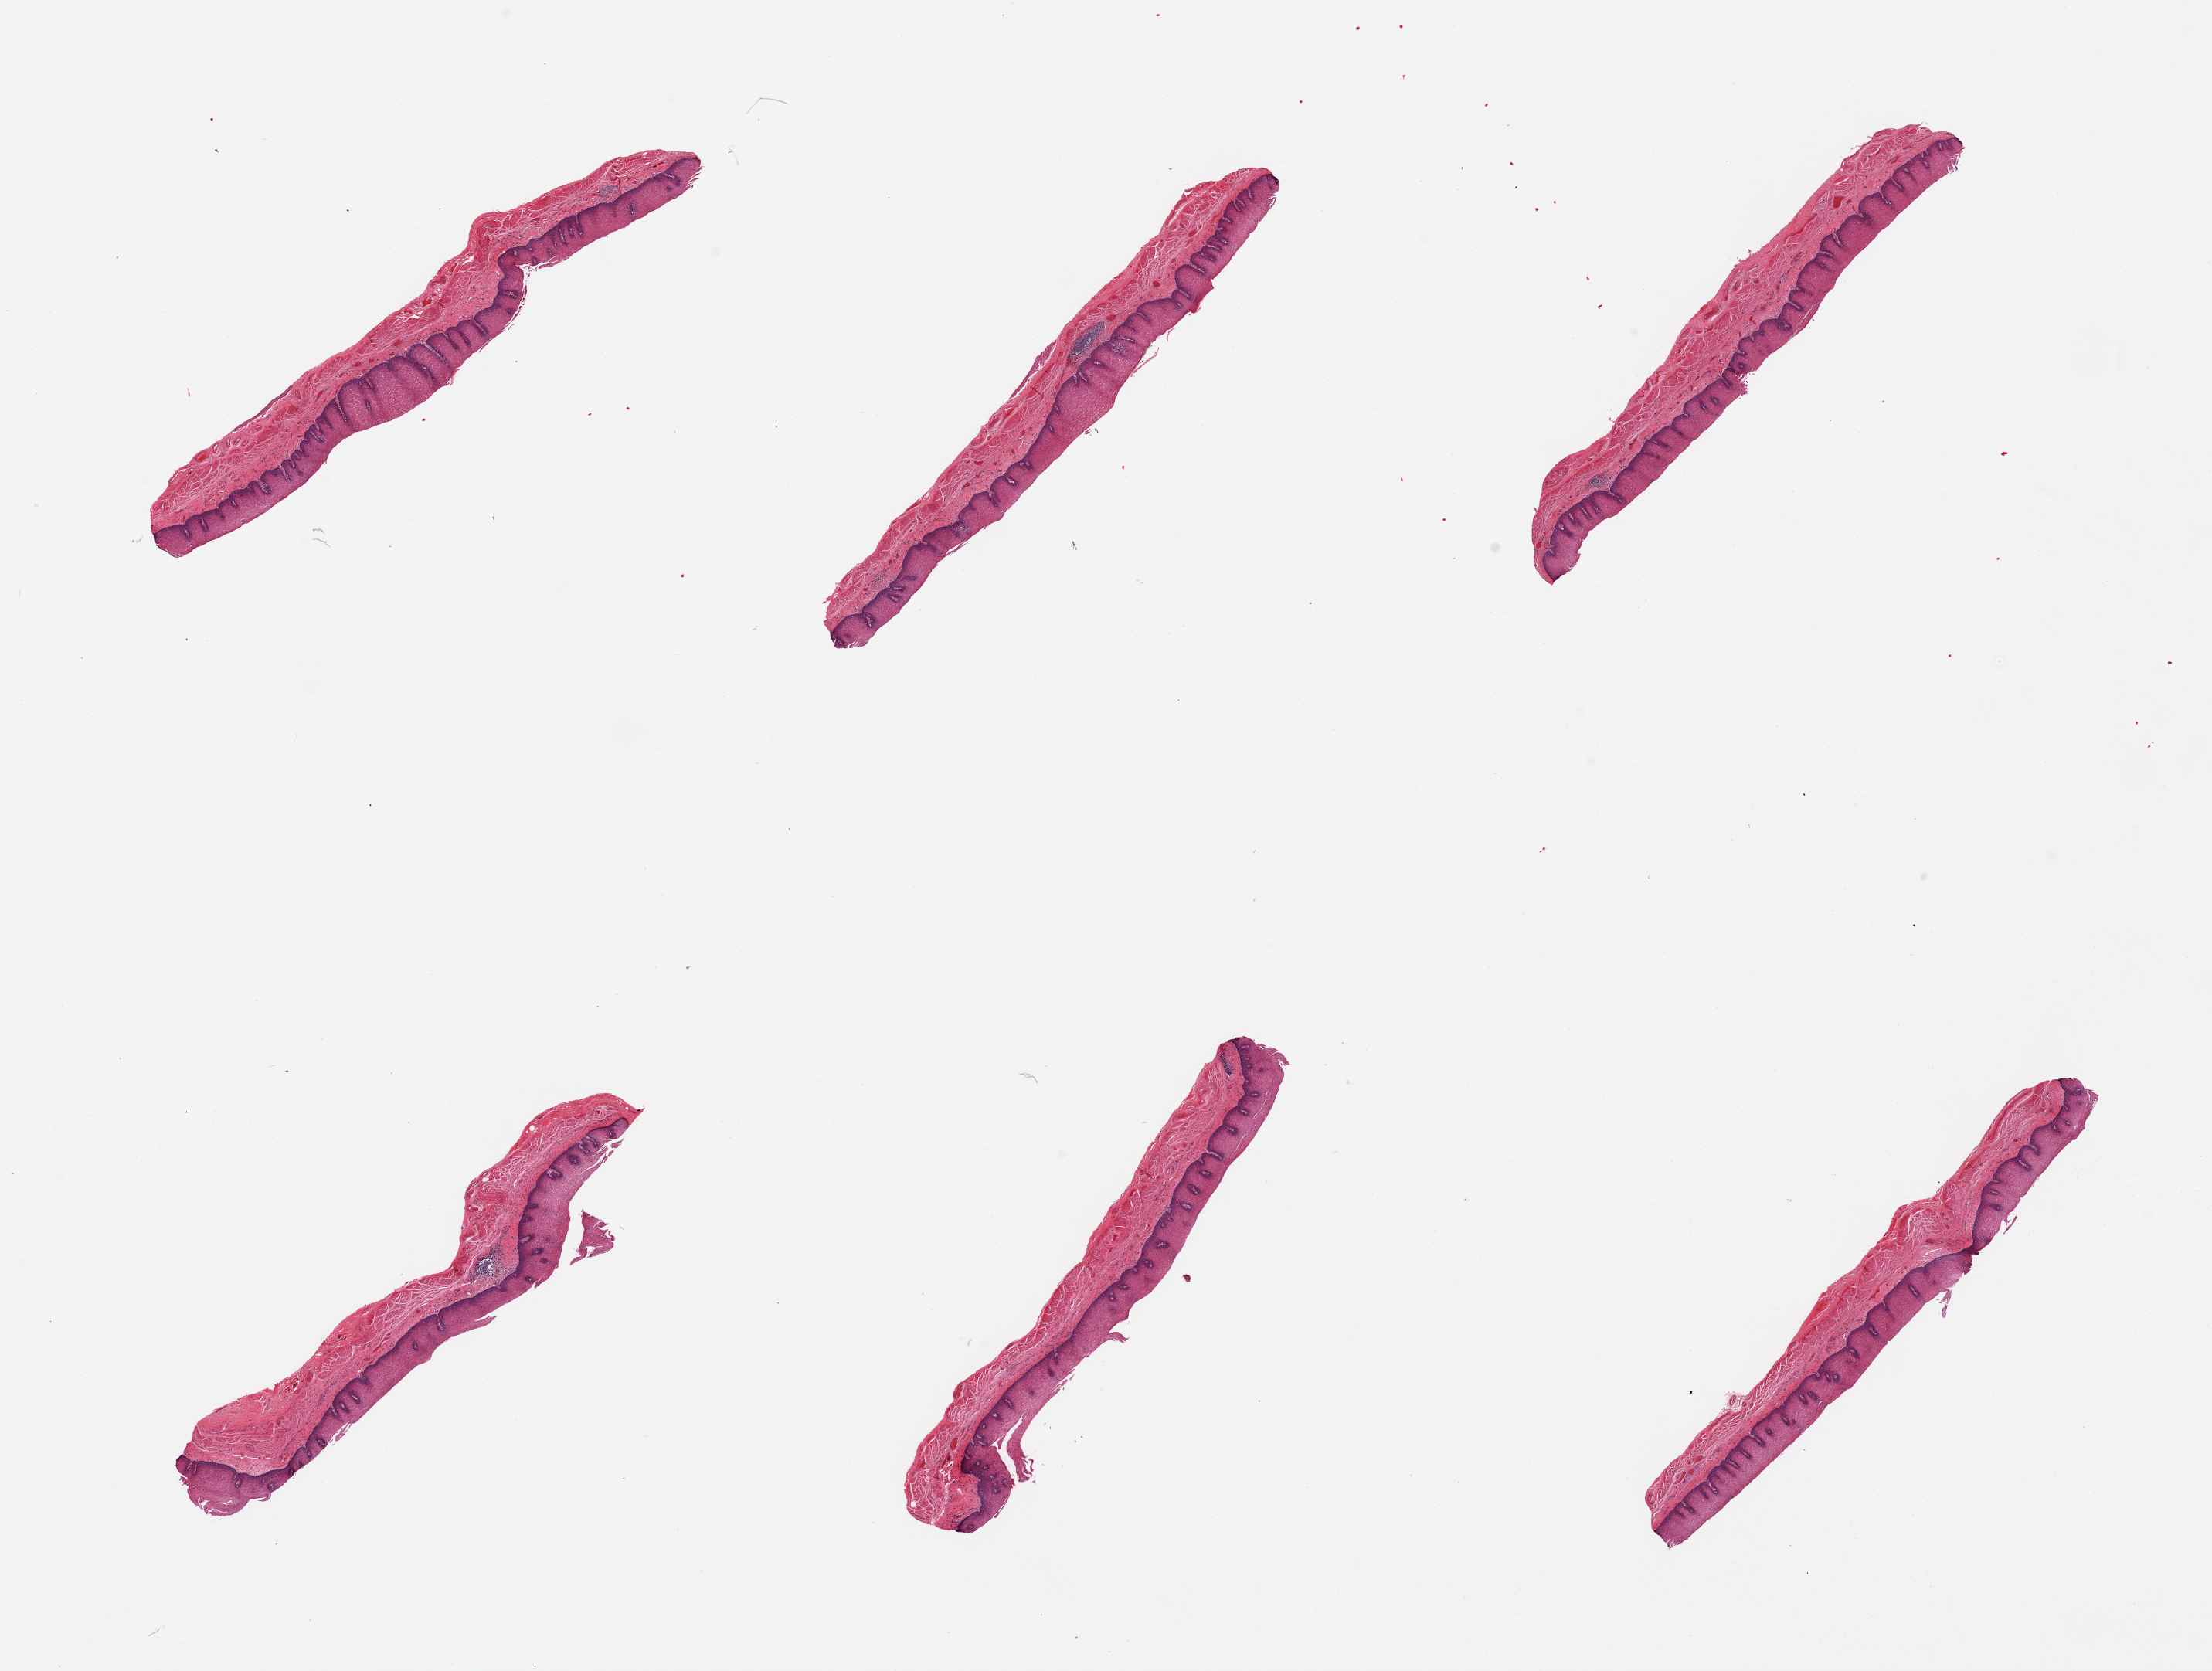
Digitized hematoxylin and eosin (H&E)-stained section, low-resolution overview of the scanned area, about 22.6 x 17.1 mm; PAXgene-fixed, paraffin-embedded tissue; sampled site (target tissue): esophageal mucous membrane; donor tissue sample. Female donor.
Review note (as recorded): 6 pieces, squamous mucosa is ~0.3-0.6 mm, ~30-70% total thickness.